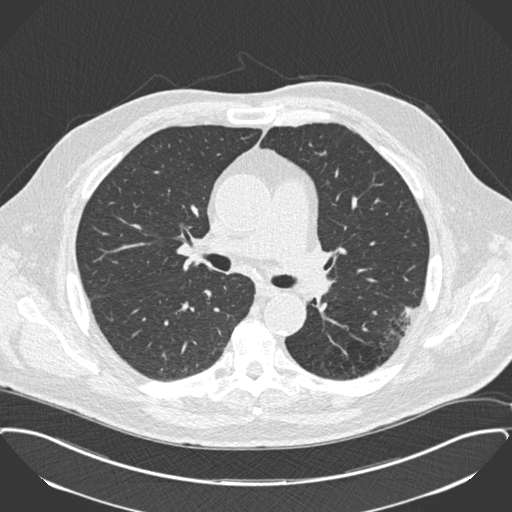
Low-dose screening chest CT, one axial slice; slice 104 of 175 in the series (ordered by position); reconstruction kernel B30f; 120 kVp; lung window (W 1500 / L -600 HU); 2 mm slice thickness; 512 × 512 image matrix.
Outlined on this slice (outlined manually by an expert reader):
- lesion 1 (tumor, lower lobe of left lung): box from (x=402, y=307) to (x=413, y=317) px